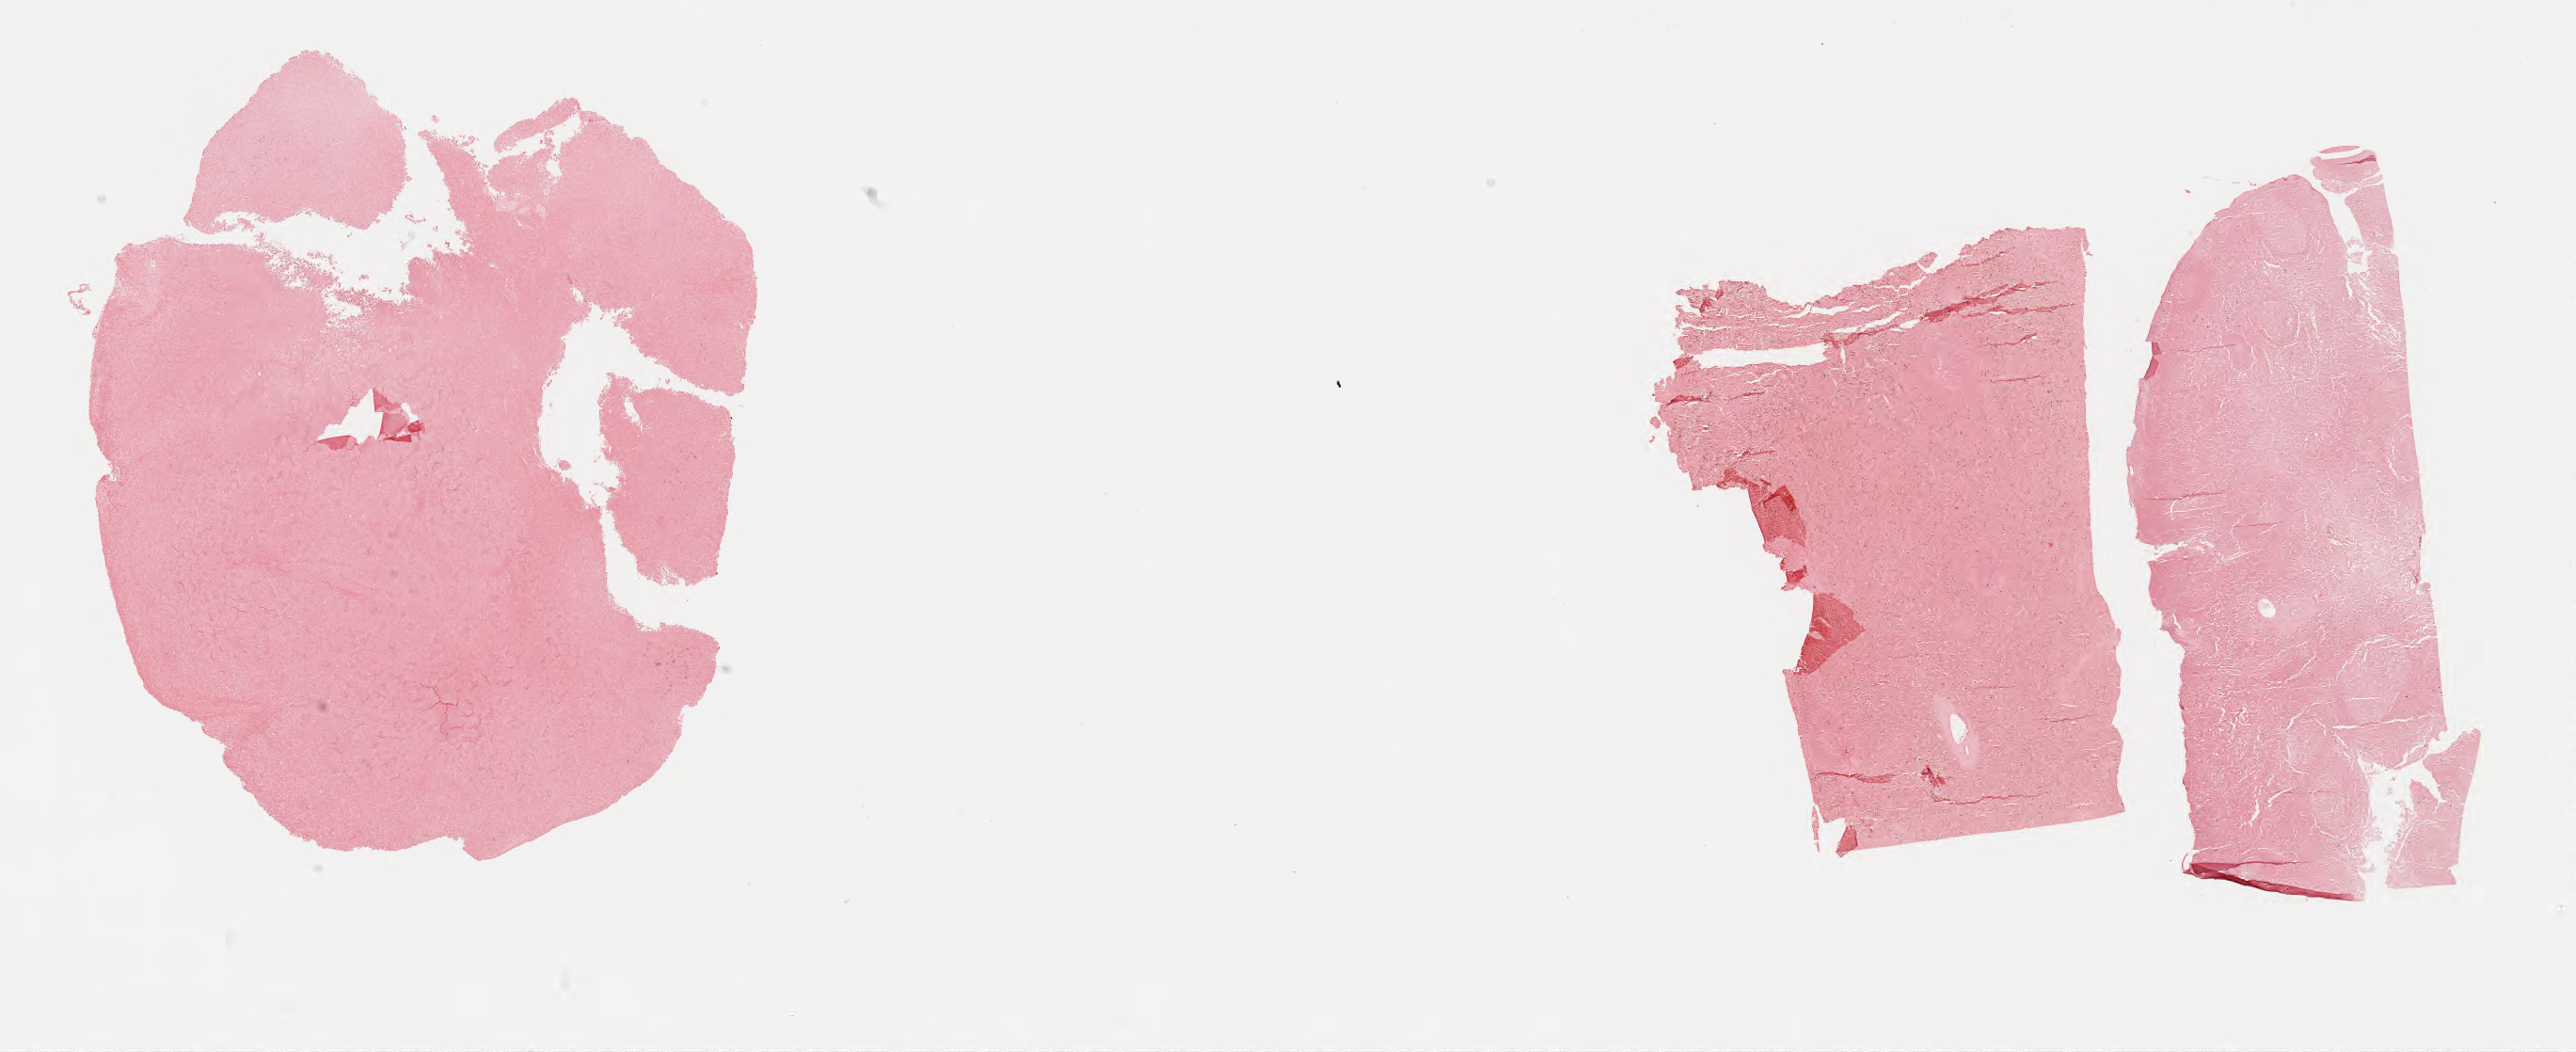
In-situ hybridisation whole-slide image, Epstein–Barr virus-encoded RNA (EBER) probe — a low-resolution overview of the entire scanned area, about 22.1 x 9.0 mm, tumor tissue, anatomic site: liver. Patient male; age 46 years.
Histologic diagnosis: Diffuse large B-cell lymphoma, NOS.